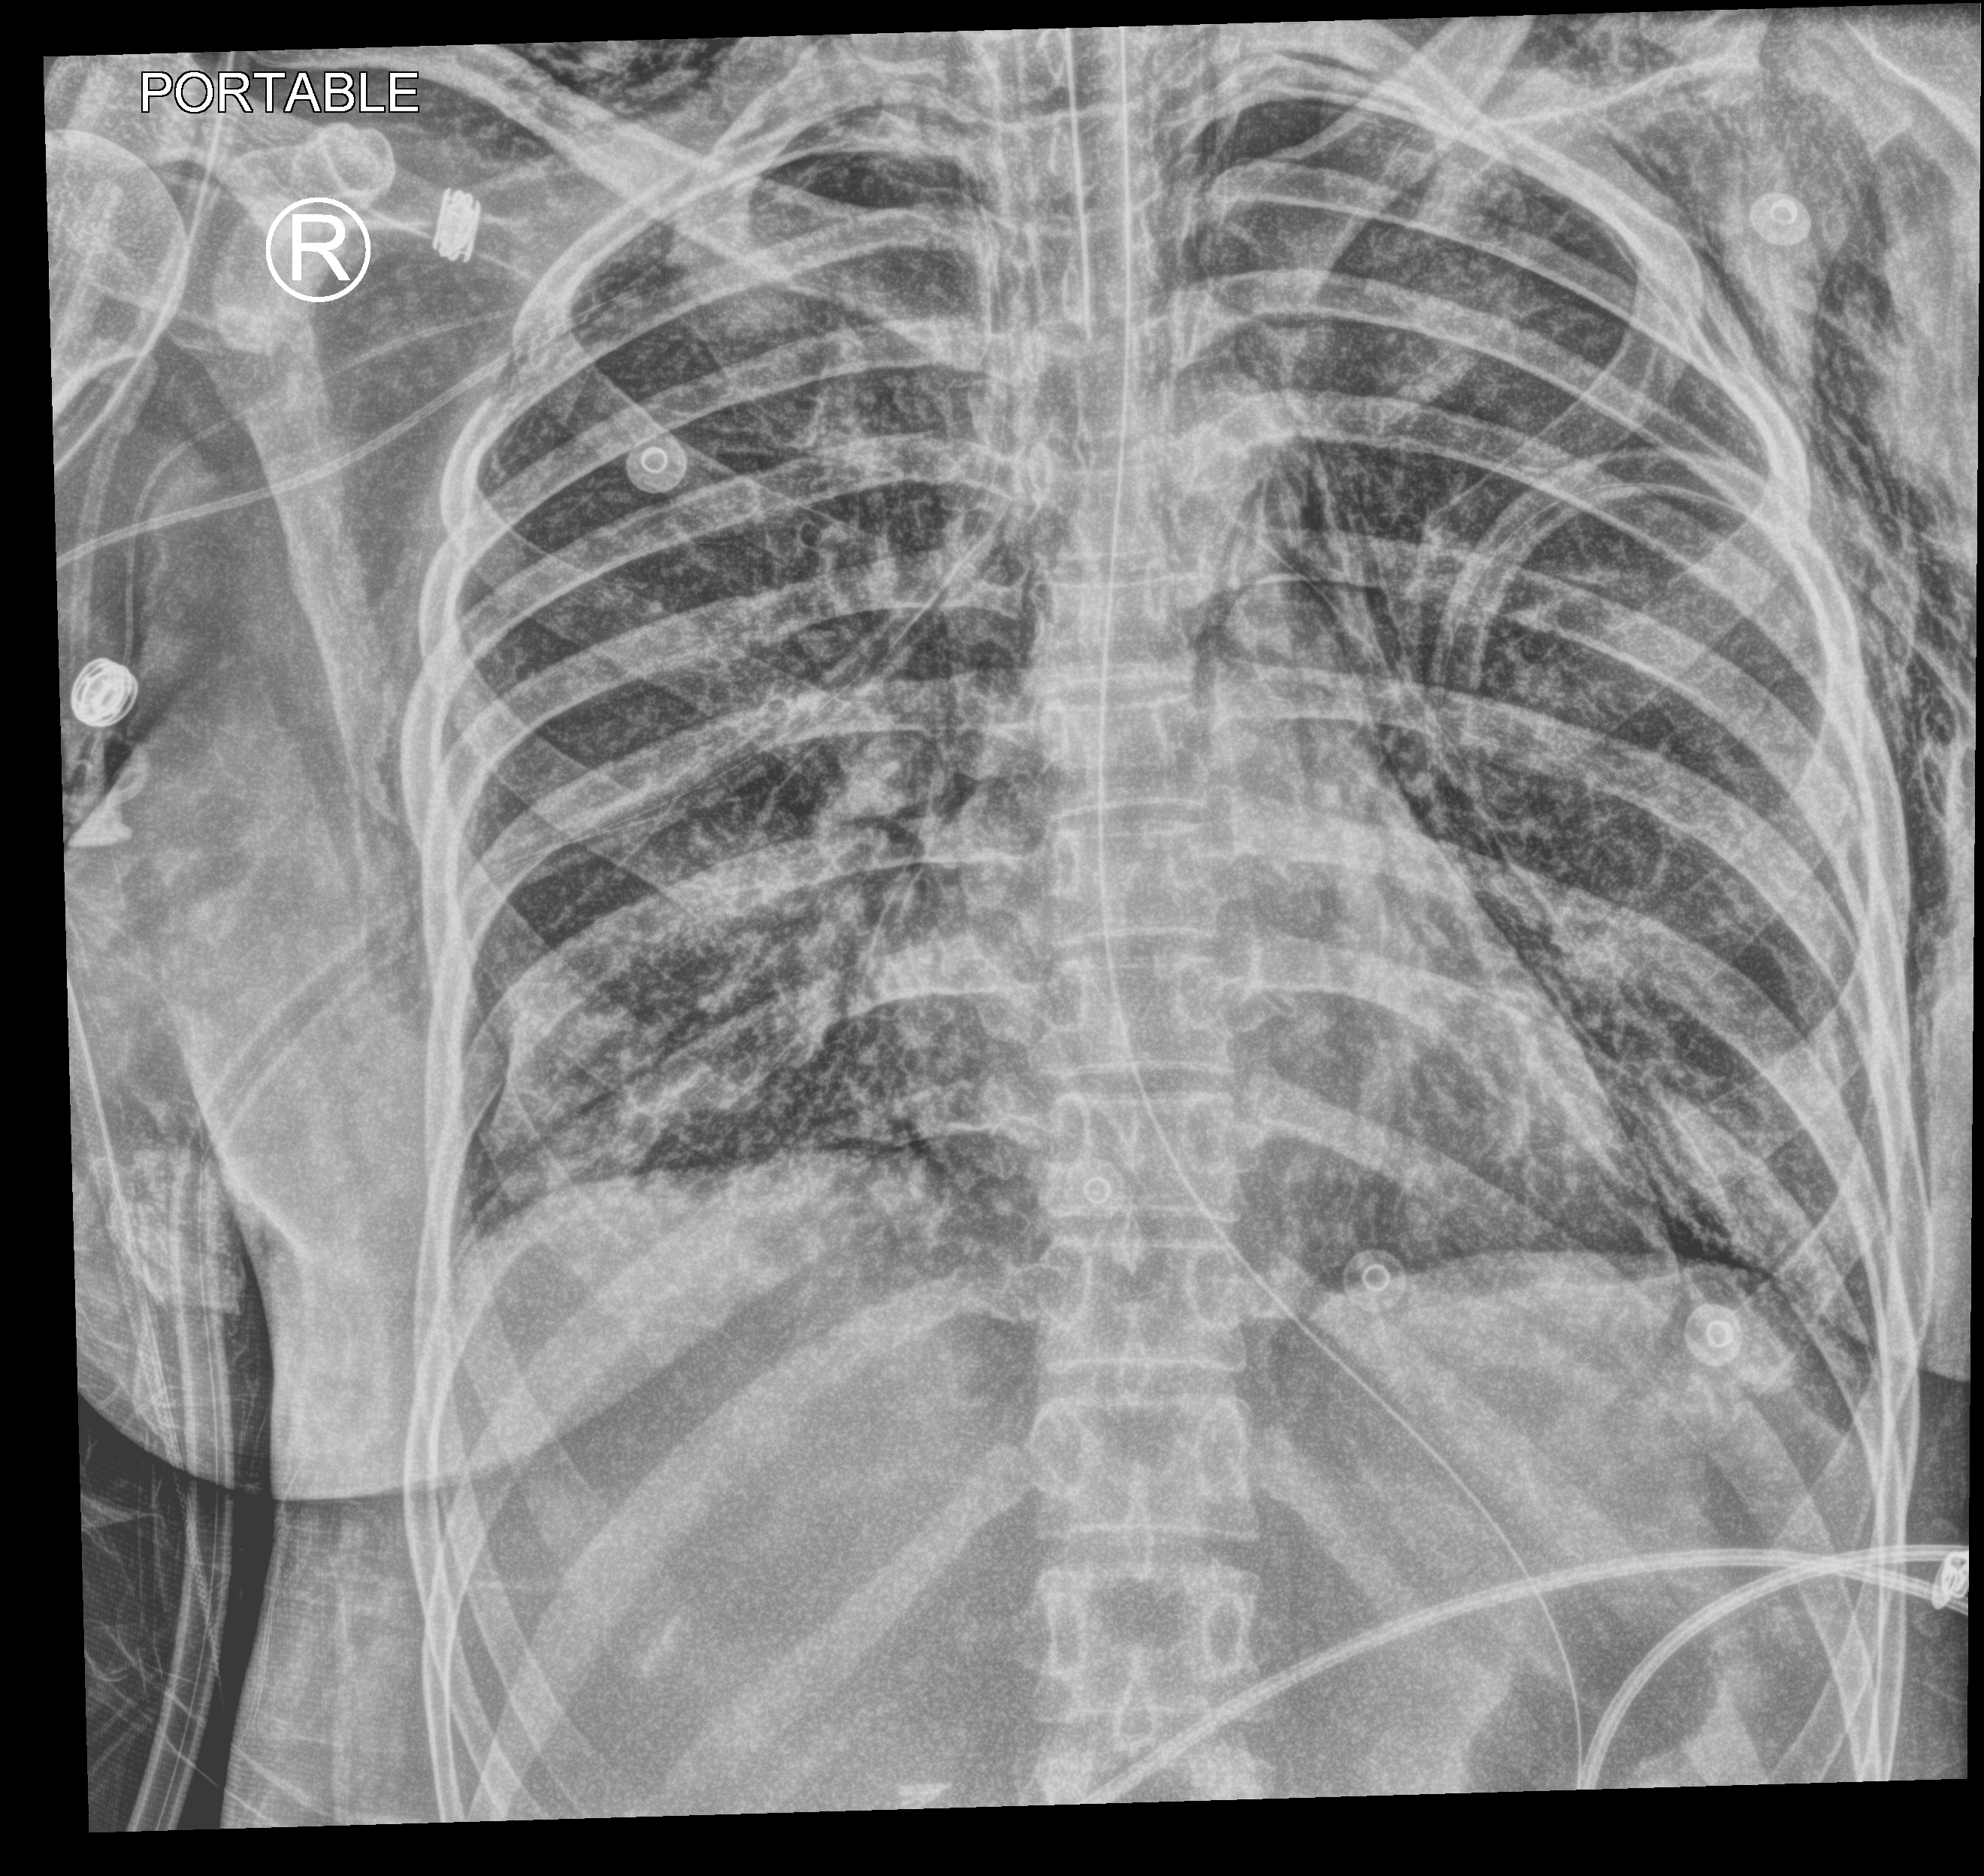
Portable chest radiograph; anteroposterior (AP) projection. Patient hospitalised with COVID-19, aged 18–59 years.
From the hospital-stay record, not from the radiograph (when in the stay this image was taken is not recorded): mechanically ventilated during this hospital stay: yes.